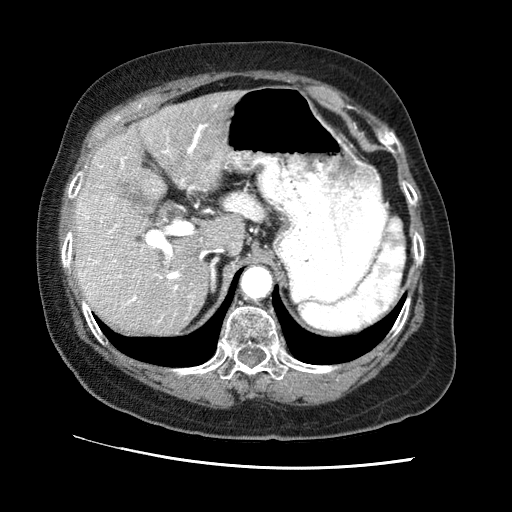
Contrast-enhanced abdominal CT (liver protocol), one axial slice. Slice 42 of 65 in the series (ordered by position). Reconstruction kernel STANDARD. 120 kVp. Soft-tissue window (W 400 / L 40 HU). 512 × 512 image matrix. From the clinical record (not read from this slice): diagnosis: hepatocellular carcinoma (patient treated with transarterial chemoembolisation; whether this scan precedes or follows treatment is not stated here); TNM stage (as recorded): Stage-II; Child-Pugh class: A; tumour nodularity: multinodular; tumour size: 2.5 cm.
Outlined on this slice (semi-automatic segmentation, software-assisted and operator-edited):
- liver parenchyma outside the tumour (the mass and vessels are separate outlines, so this box may not span the whole liver): bounding box (x1, y1, x2, y2) in pixels: (76, 90, 244, 334)
- liver vessels: (82, 124, 214, 305)